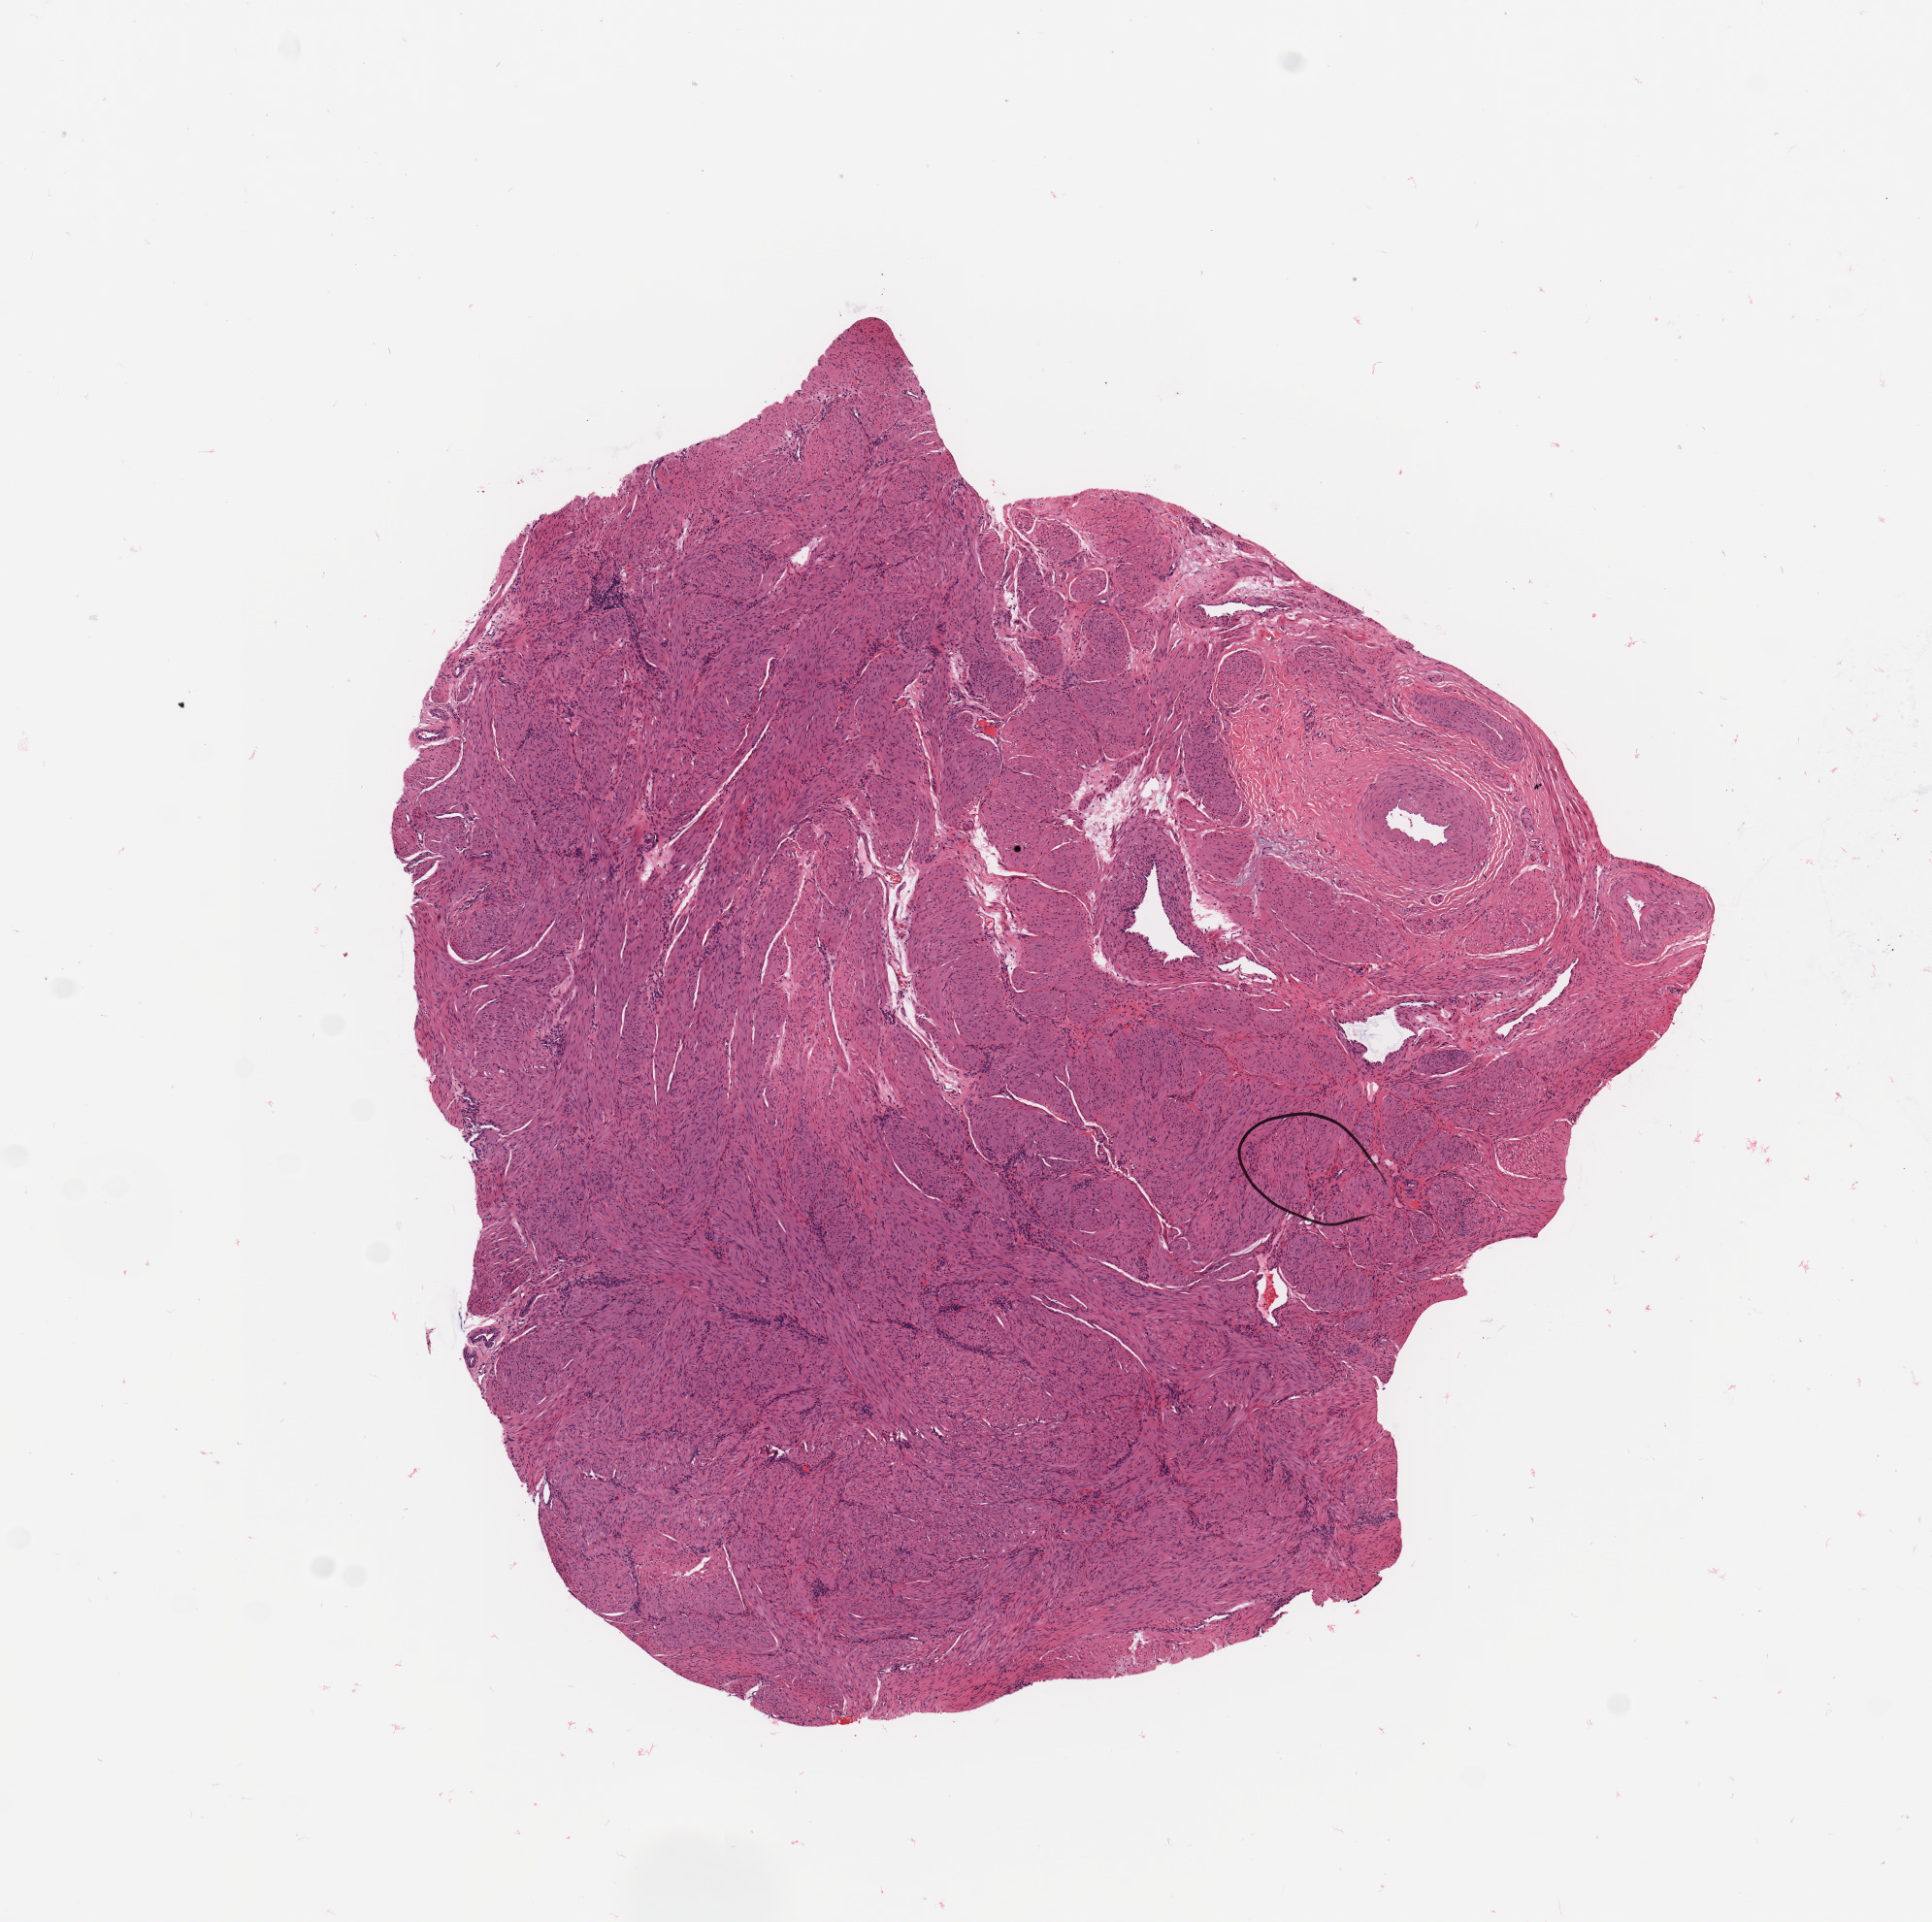
H&E whole-slide image — whole scanned area (about 7.9 x 7.8 mm) shown as a low-resolution overview; normal (non-tumour) tissue sample, uterus. Patient: female, age 56 years.
This section: normal (non-tumour) tissue from the same patient. Patient diagnosis: Endometrioid adenocarcinoma, NOS.